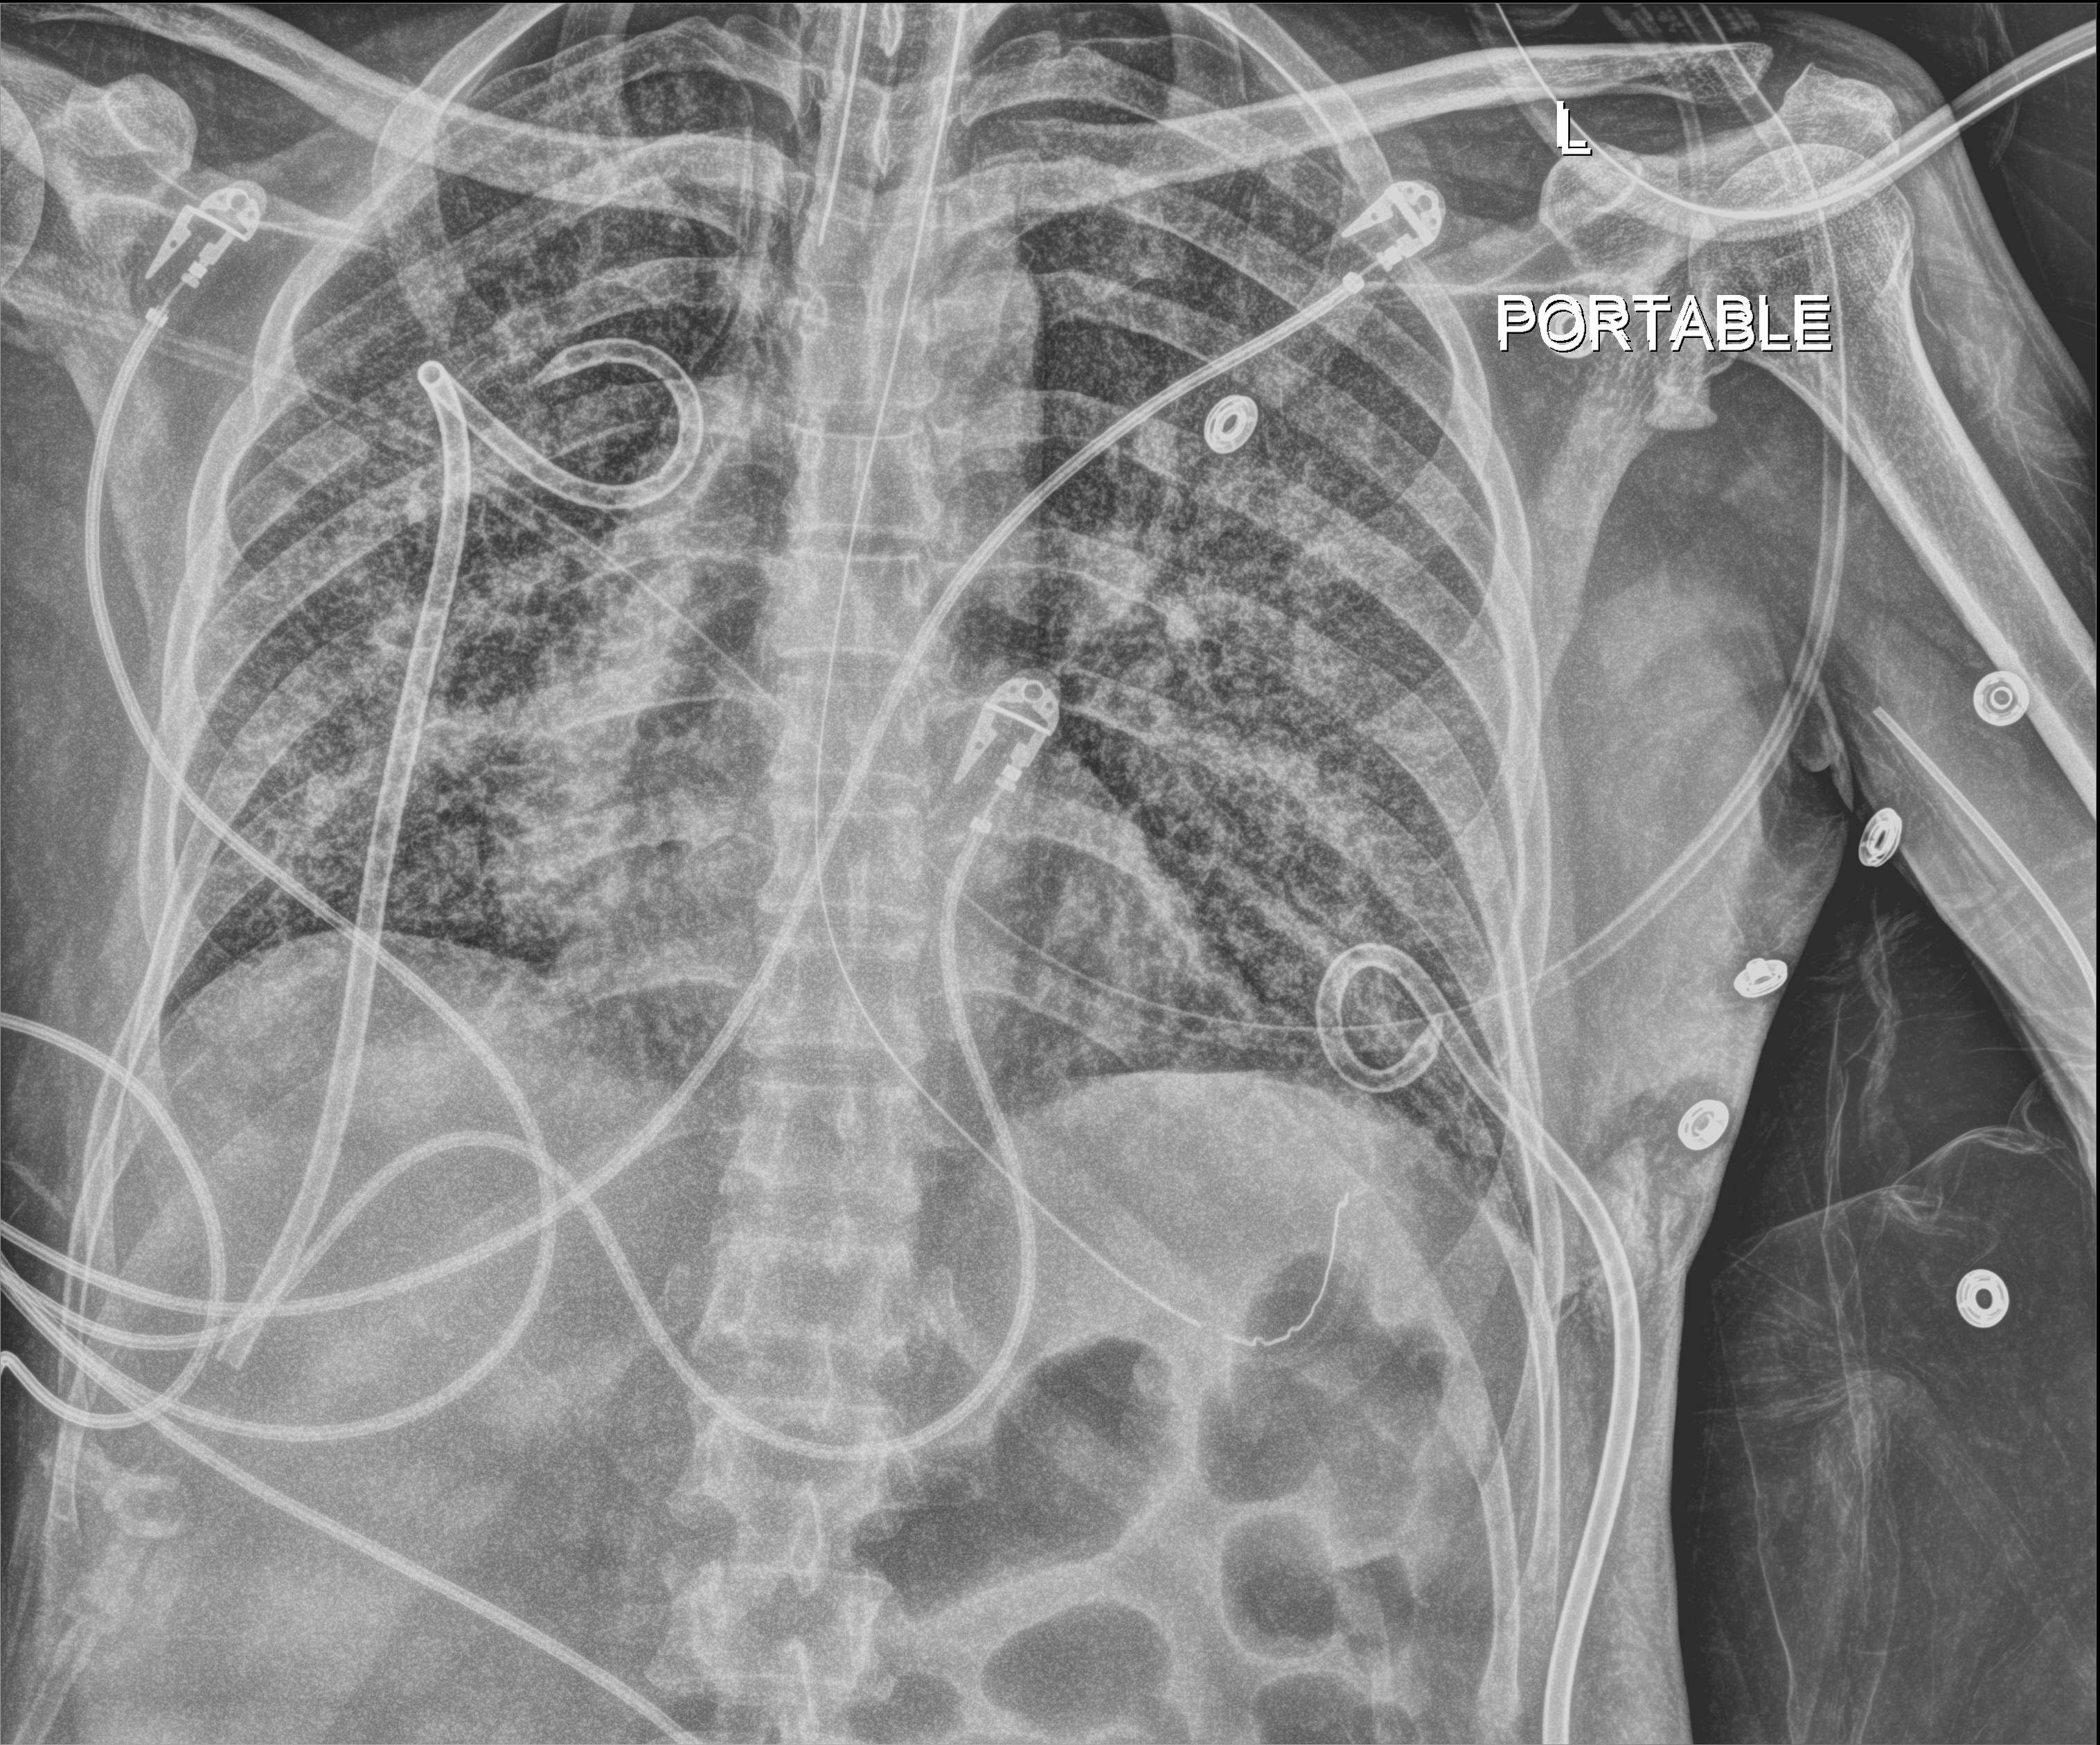
Chest radiograph (digital radiography), anteroposterior (AP) projection. Adult patient hospitalised with COVID-19, age 18–59 years.
Hospital-stay facts (about this admission, not read from this image; timing relative to this image not recorded):
- chronic kidney disease (admission record): no